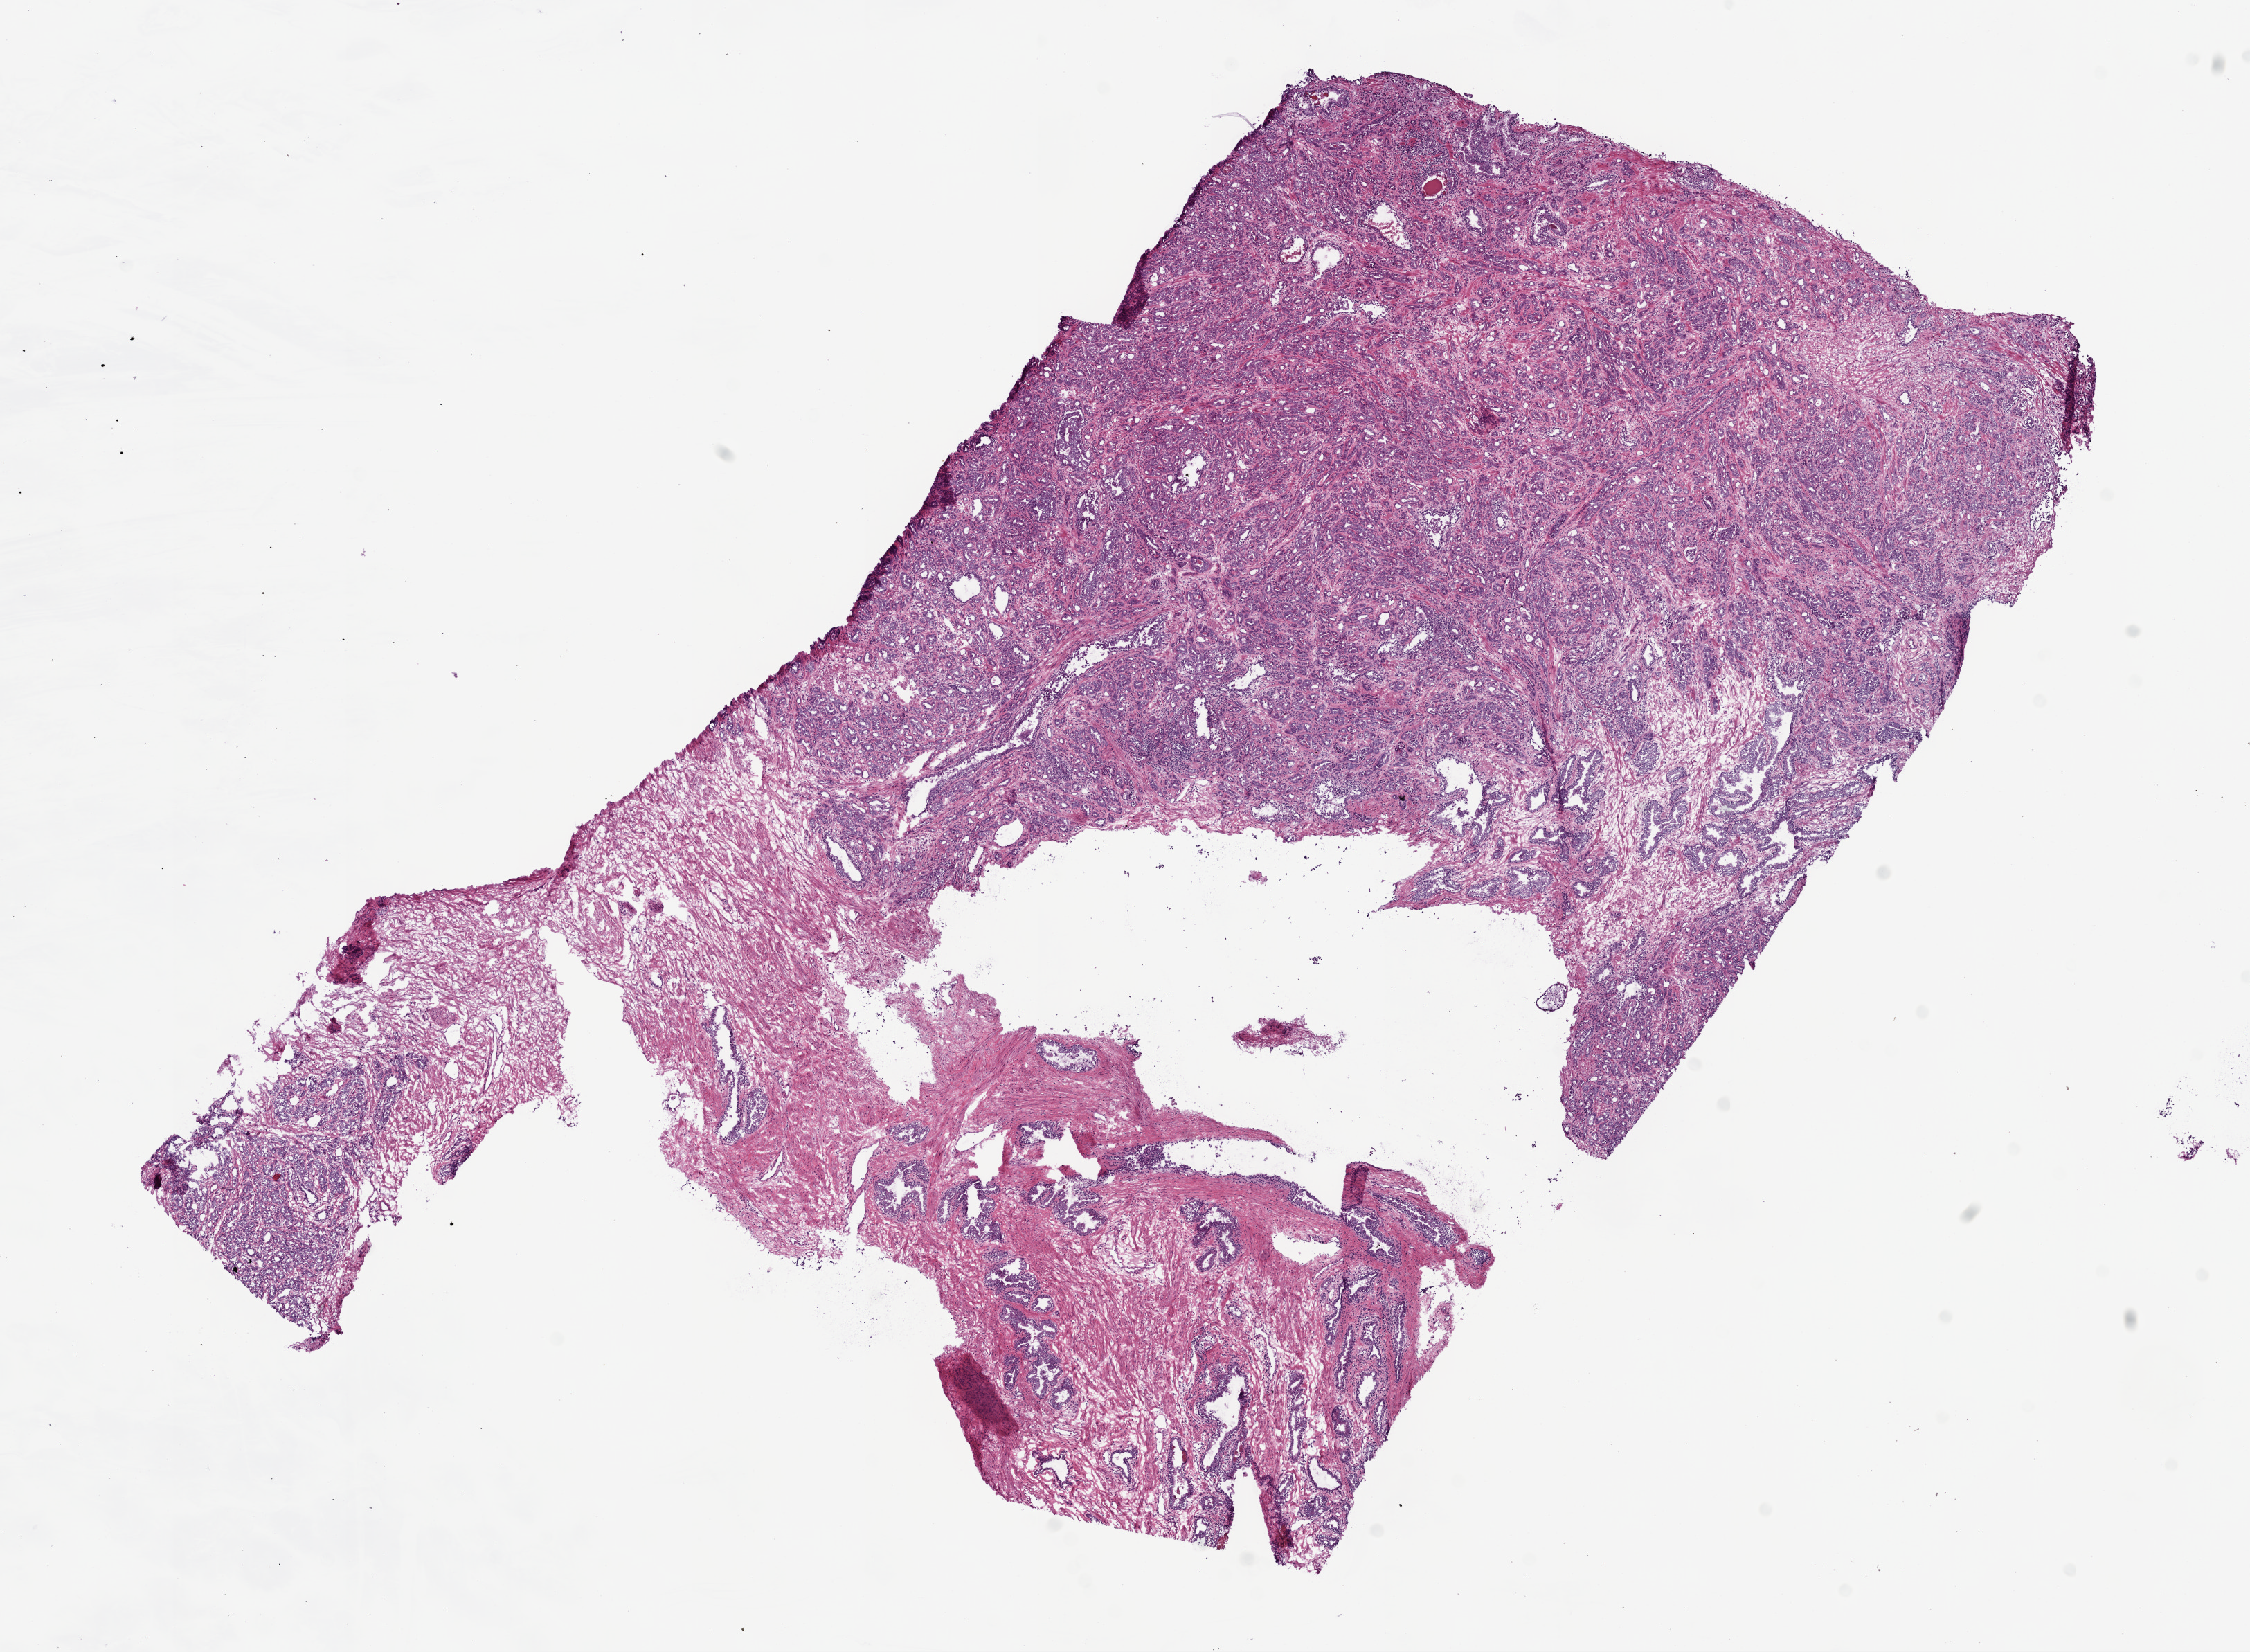
Digitized Hematoxylin and eosin (H&E) stained tissue section (whole slide) — shown as a low-resolution overview of the whole scanned area (about 13.0 x 9.6 mm, from a 20x scan), frozen section, prostate, primary tumour sample. Male patient; age at initial diagnosis 55 years. Gleason score: 7 (4+3). Slide review estimates, as recorded: tumour cells 60%, tumour nuclei 75%, normal cells 15%, stromal cells 25%, necrosis 0%. Infiltration values recorded for this section: lymphocyte infiltration 1%, monocyte infiltration 0%, neutrophil infiltration 0%.
Diagnosis: Acinar cell carcinoma (prostate gland).